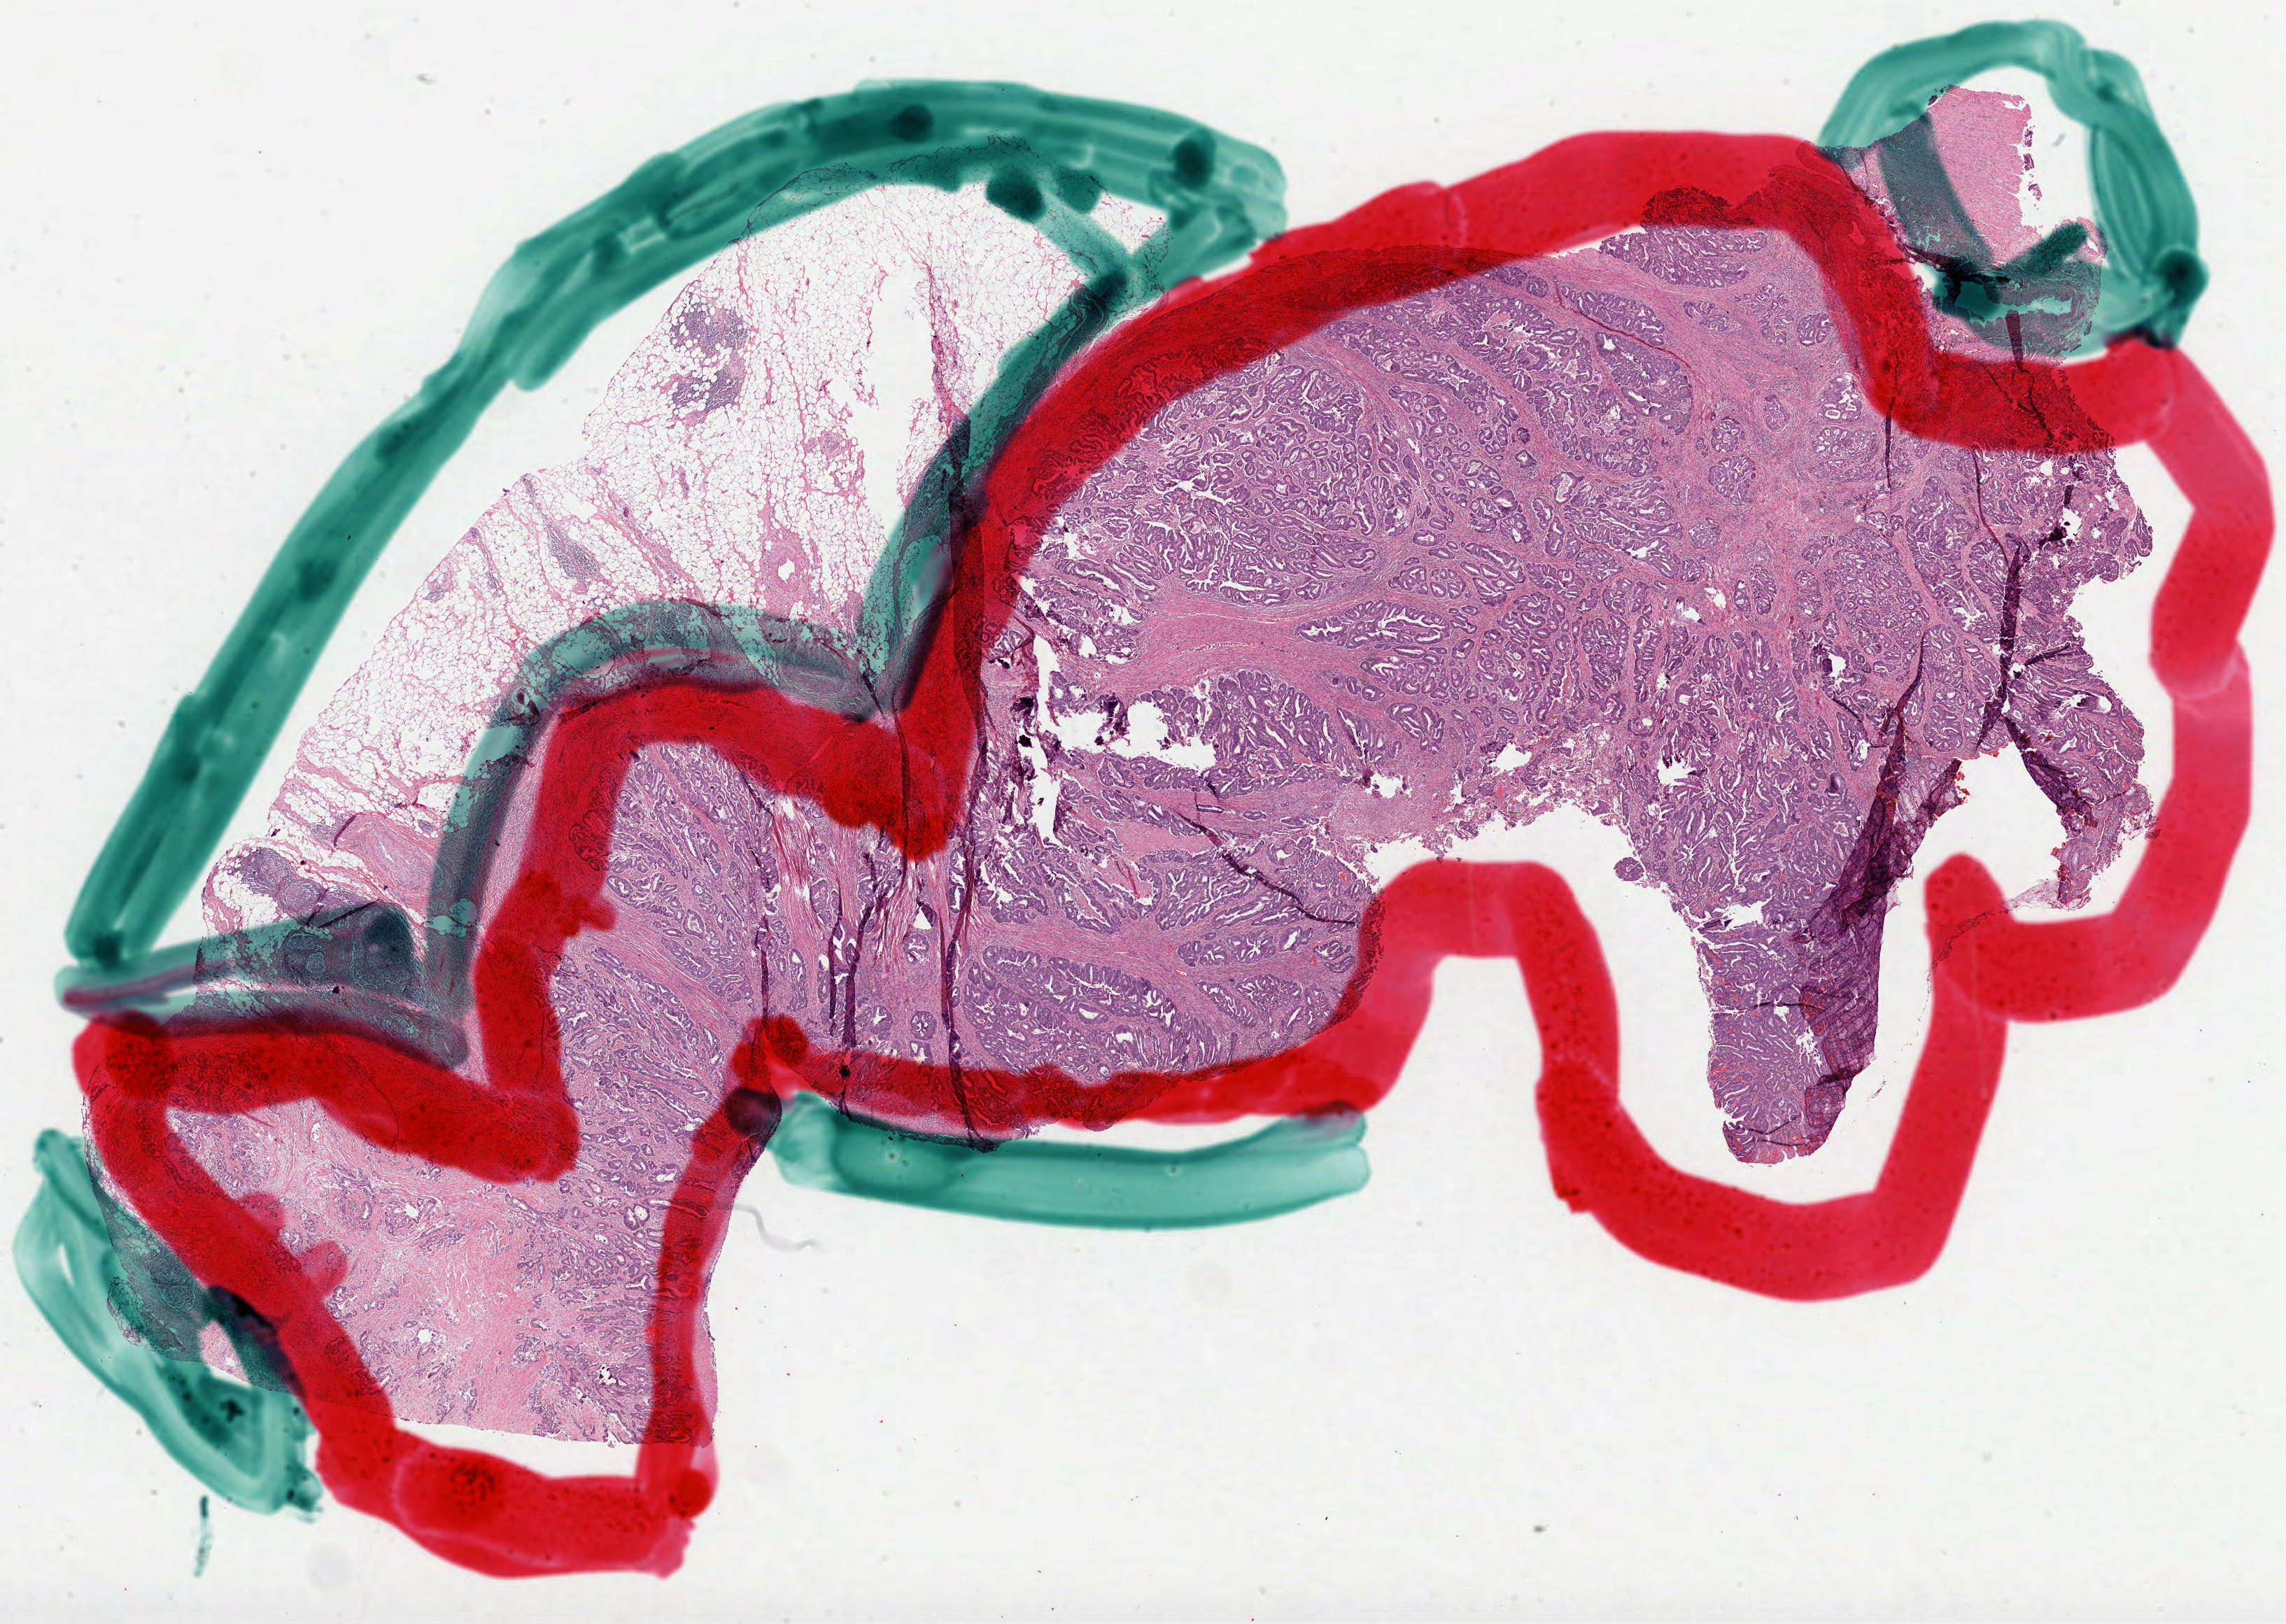
Whole-slide histology image, Hematoxylin and eosin (H&E) stained — whole scanned area (about 26.3 x 18.7 mm, slide scanned at 40x) shown as a low-resolution overview; FFPE section; sample: primary tumour, rectum. Male, age 70 years at initial diagnosis.
Pathologic diagnosis: Adenocarcinoma, NOS (connective, subcutaneous and other soft tissues of abdomen). Lymph nodes positive (case pathology): 12 of 12 examined. AJCC pathologic stage: IIIC (7th edition).